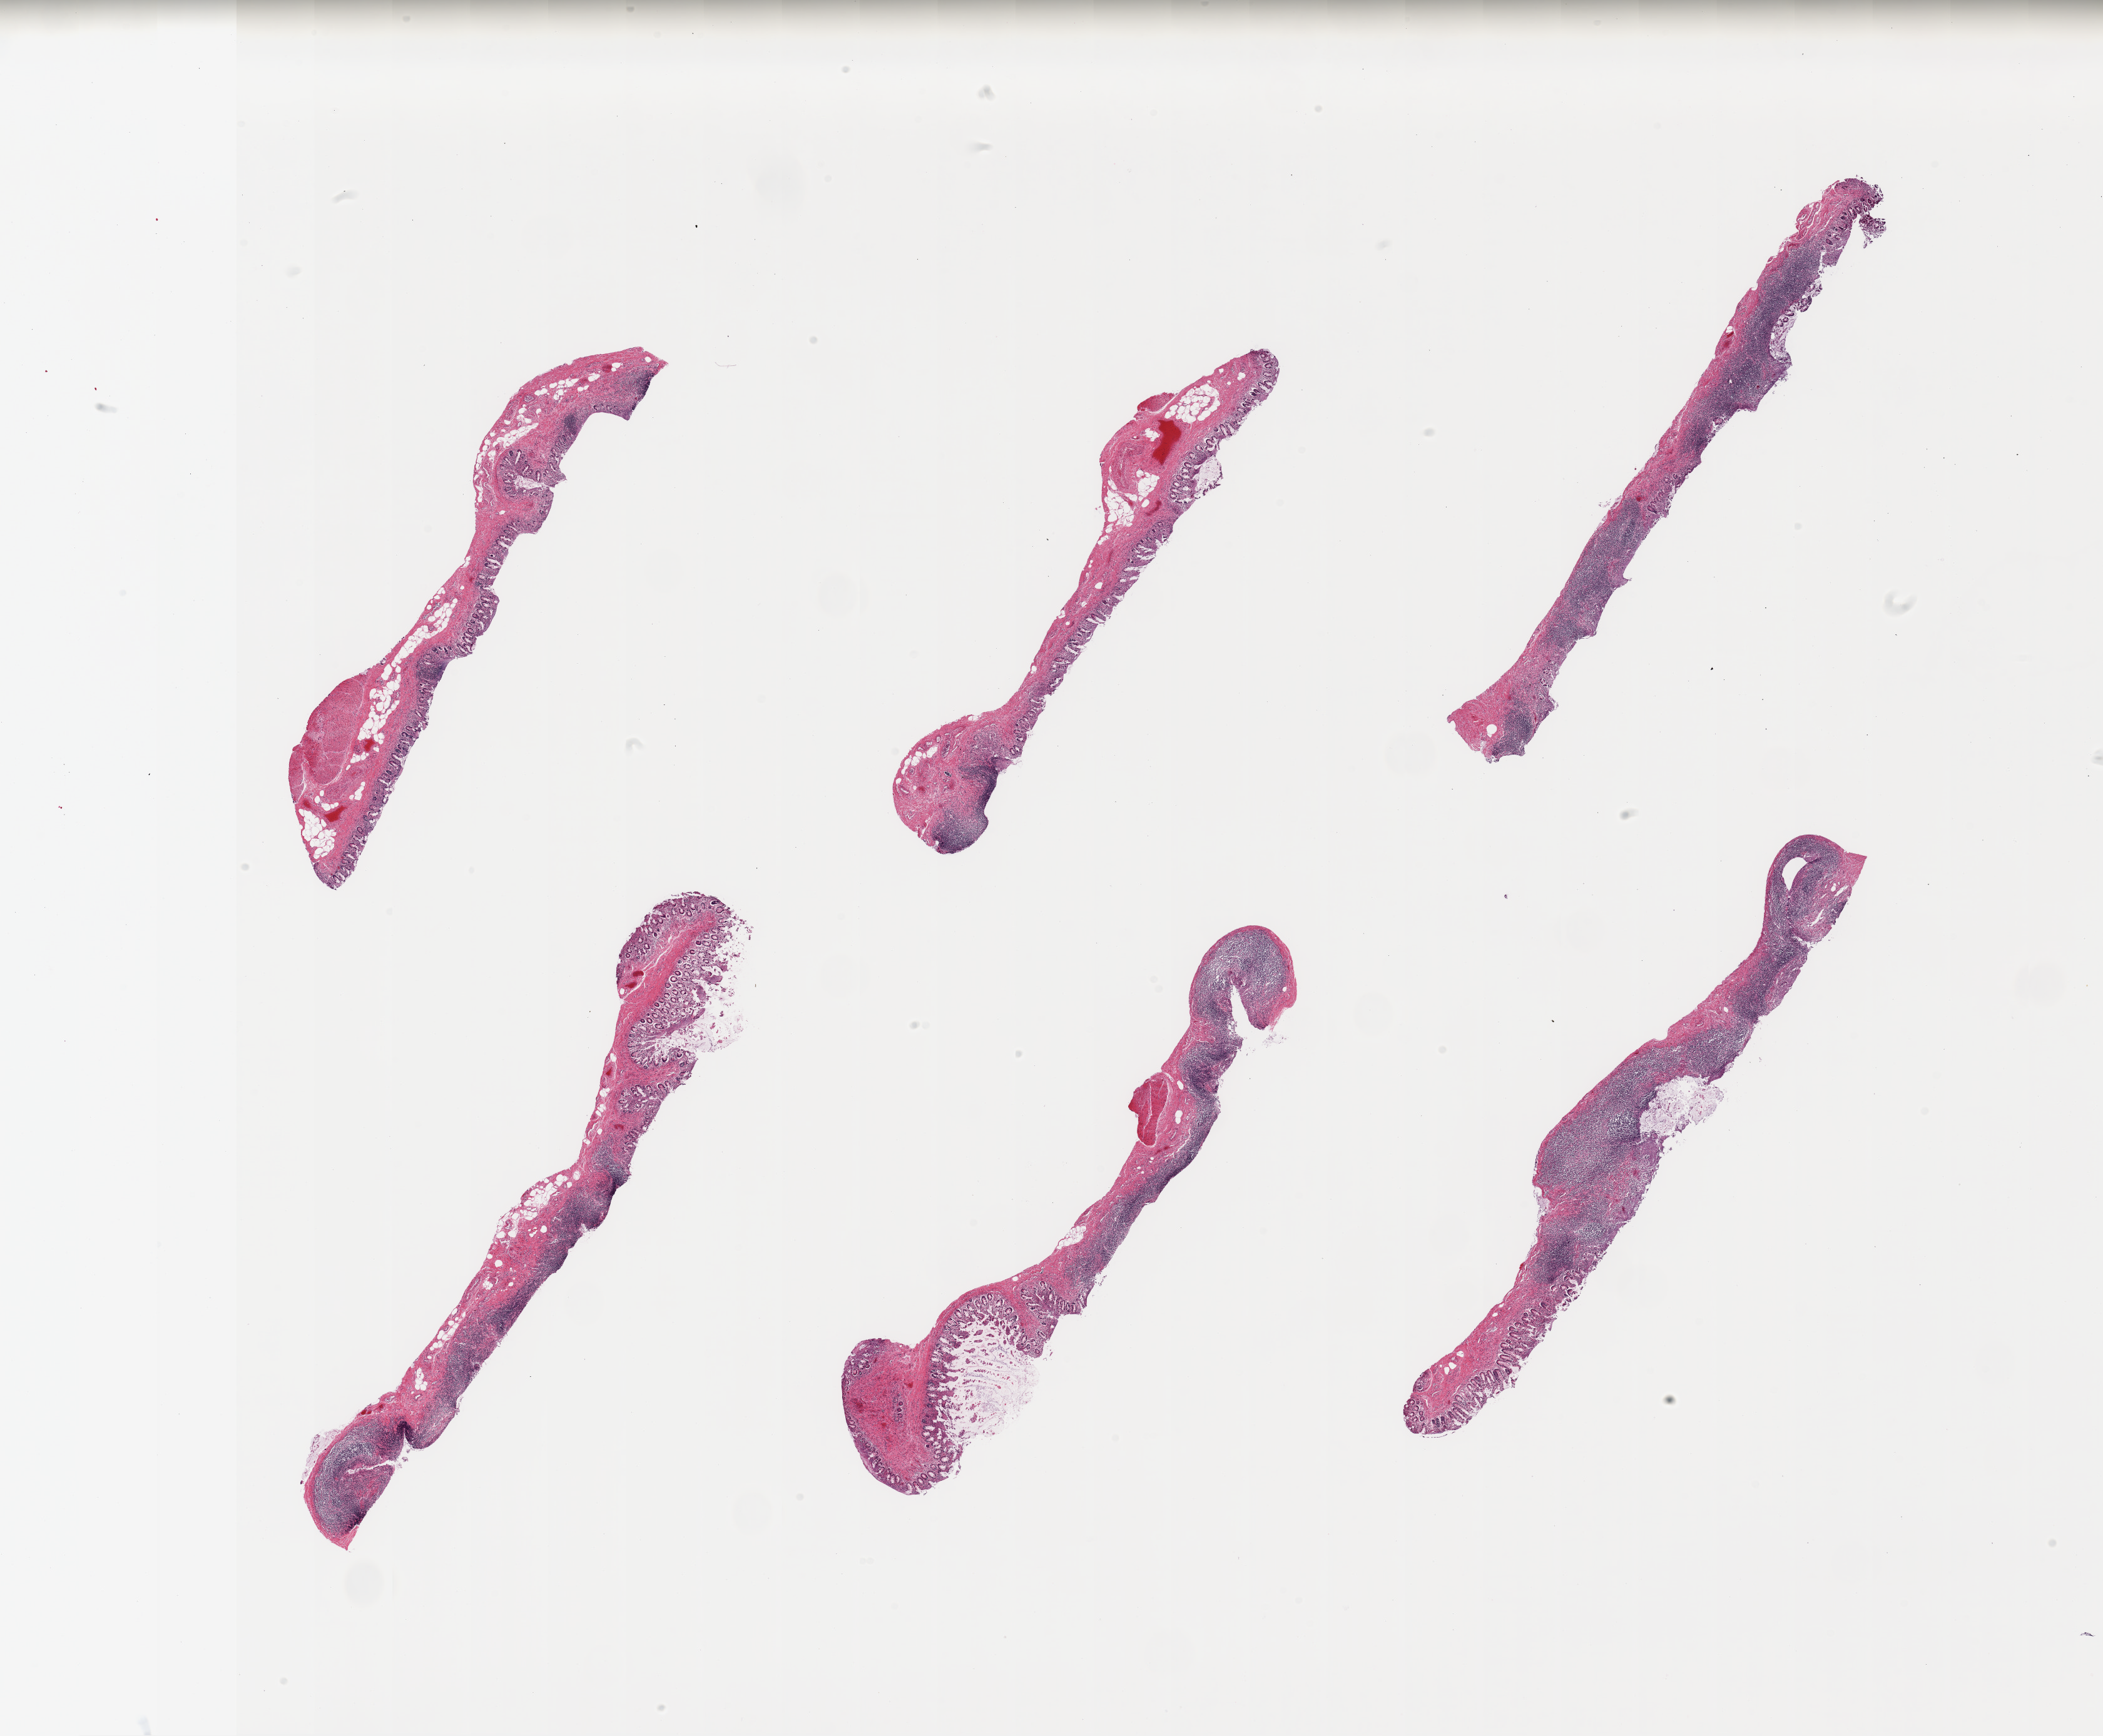
Hematoxylin and eosin (H&E) whole-slide image — a low-resolution overview of the entire scanned area, about 26.6 x 21.9 mm (acquisition: 20x scan); PAXgene-fixed, paraffin-embedded tissue; section of ileum (target tissue); tissue donor sample. Donor sex: male.
• pathologist's review note for this sample: 6 pieces; abundant lymphoid tissue; well dissected mucosa and submucosa